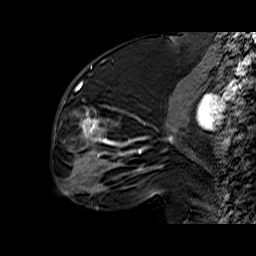
Breast MRI (dynamic contrast-enhanced), one sagittal slice. Slice 25 of 60 in the series (ordered by position). Dynamic contrast-enhanced series, time point 2 of 6 at this slice position (early post-contrast). 1.5 T. TE 6.4 ms, TR 32.9 ms. 256 × 256 image matrix, field of view 200 × 200 mm. Female patient. From the clinical record (not read from this slice): setting: breast cancer imaged before/during neoadjuvant chemotherapy; receptor status: triple-negative.
Annotated regions visible in this slice (semi-automatically segmented with operator editing):
- analysis volume of interest (the breast-tissue region the enhancement analysis was run in; not a lesion): bounding box (x1, y1, x2, y2) in pixels: (57, 65, 159, 174)
- tumour enhancement mask (voxels above the 100 % enhancement threshold inside the analysis volume of interest): (71, 83, 159, 171)